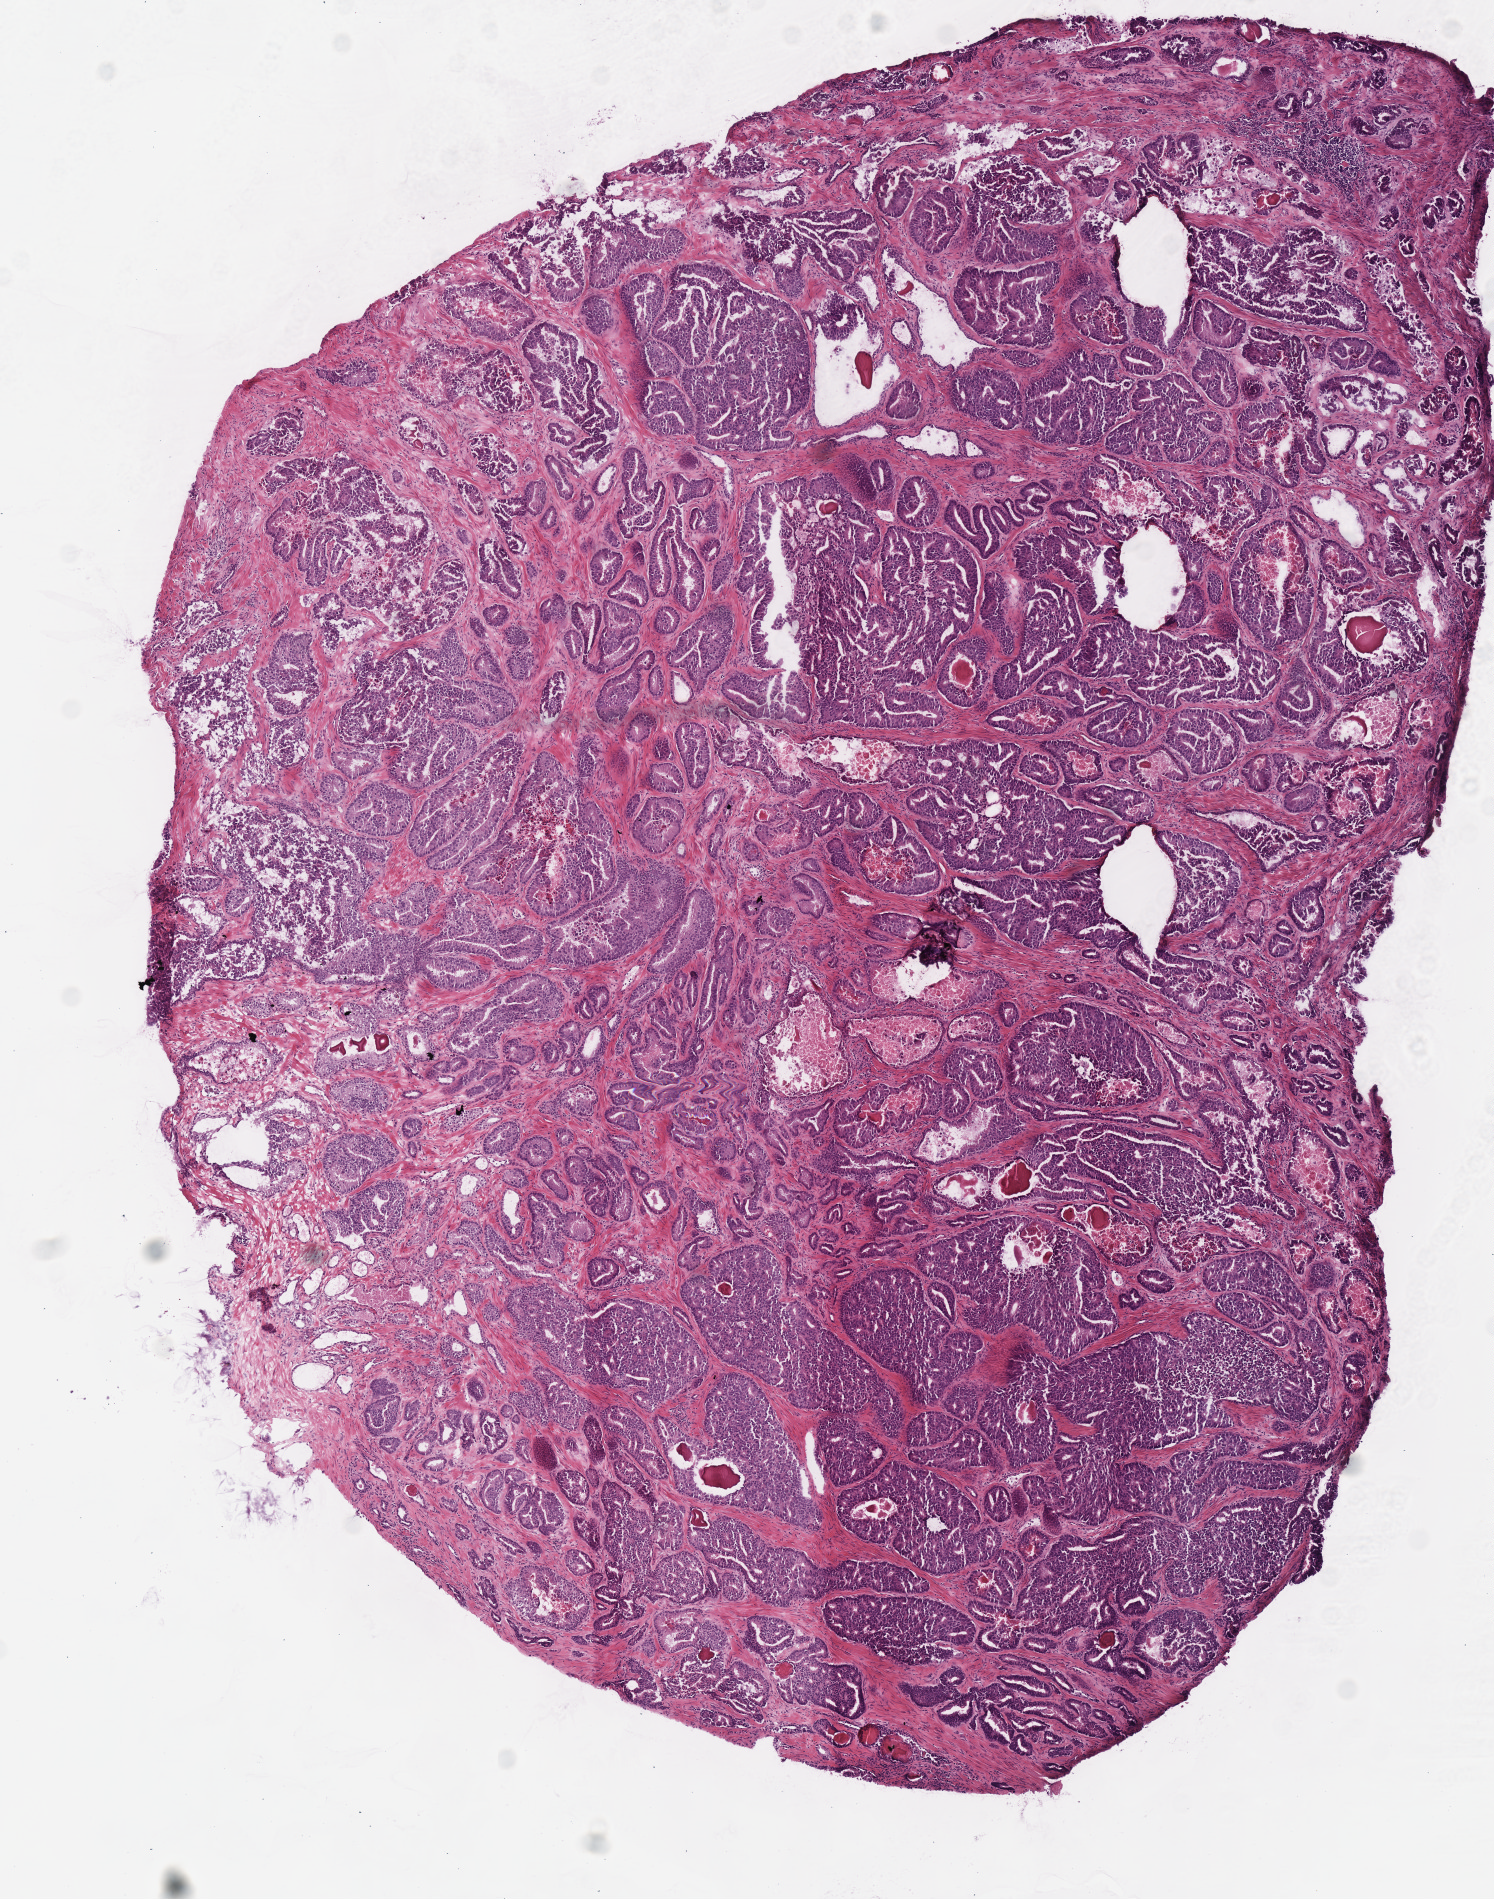
Whole-slide histology image, H&E-stained — low-resolution overview of the scanned area, about 5.9 x 7.5 mm (acquisition: 40x scan), frozen section from the top of the tissue portion, primary tumour sample from the prostate. Patient: male, age at initial diagnosis 46 years. Gleason score: 7 (4+3). Composition of this section per pathologist review: tumour nuclei 60%, necrosis 0%.
- histologic diagnosis: Acinar cell carcinoma (prostate gland)
- laterality: bilateral
- lymph nodes positive (case pathology): 0 of 8 examined